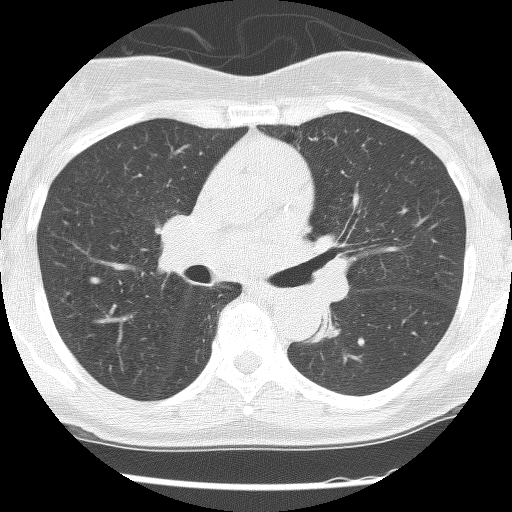
Axial slice from a low-dose chest CT screening exam; second screening round (one year after baseline); lung window (W 1500 / L -600 HU); lung (sharp) reconstruction kernel (BONE); 120 kVp; 512 × 512 image matrix, field of view 290 × 290 mm. Female participant, aged 62 years at enrolment. Former smoker at enrolment.
• Expert reader's lesion annotation, bounding box (x1, y1, x2, y2) in pixels: (299, 300, 351, 349).
• Screening reader's record for this exam (one nodule recorded; not confirmed to be the boxed lesion): non-calcified nodule or mass ≥4 mm, right upper lobe, 30 × 30 mm, poorly defined margins, ground glass attenuation, pre-existing on the prior screen: yes; interval growth: no.
• Note: the box lies in the patient's left hemithorax on this image, whereas the reader's record names the right lung; they may be different findings.
• Official screen result: positive, no significant change: stable abnormalities potentially related to lung cancer, unchanged since the prior screening exam.